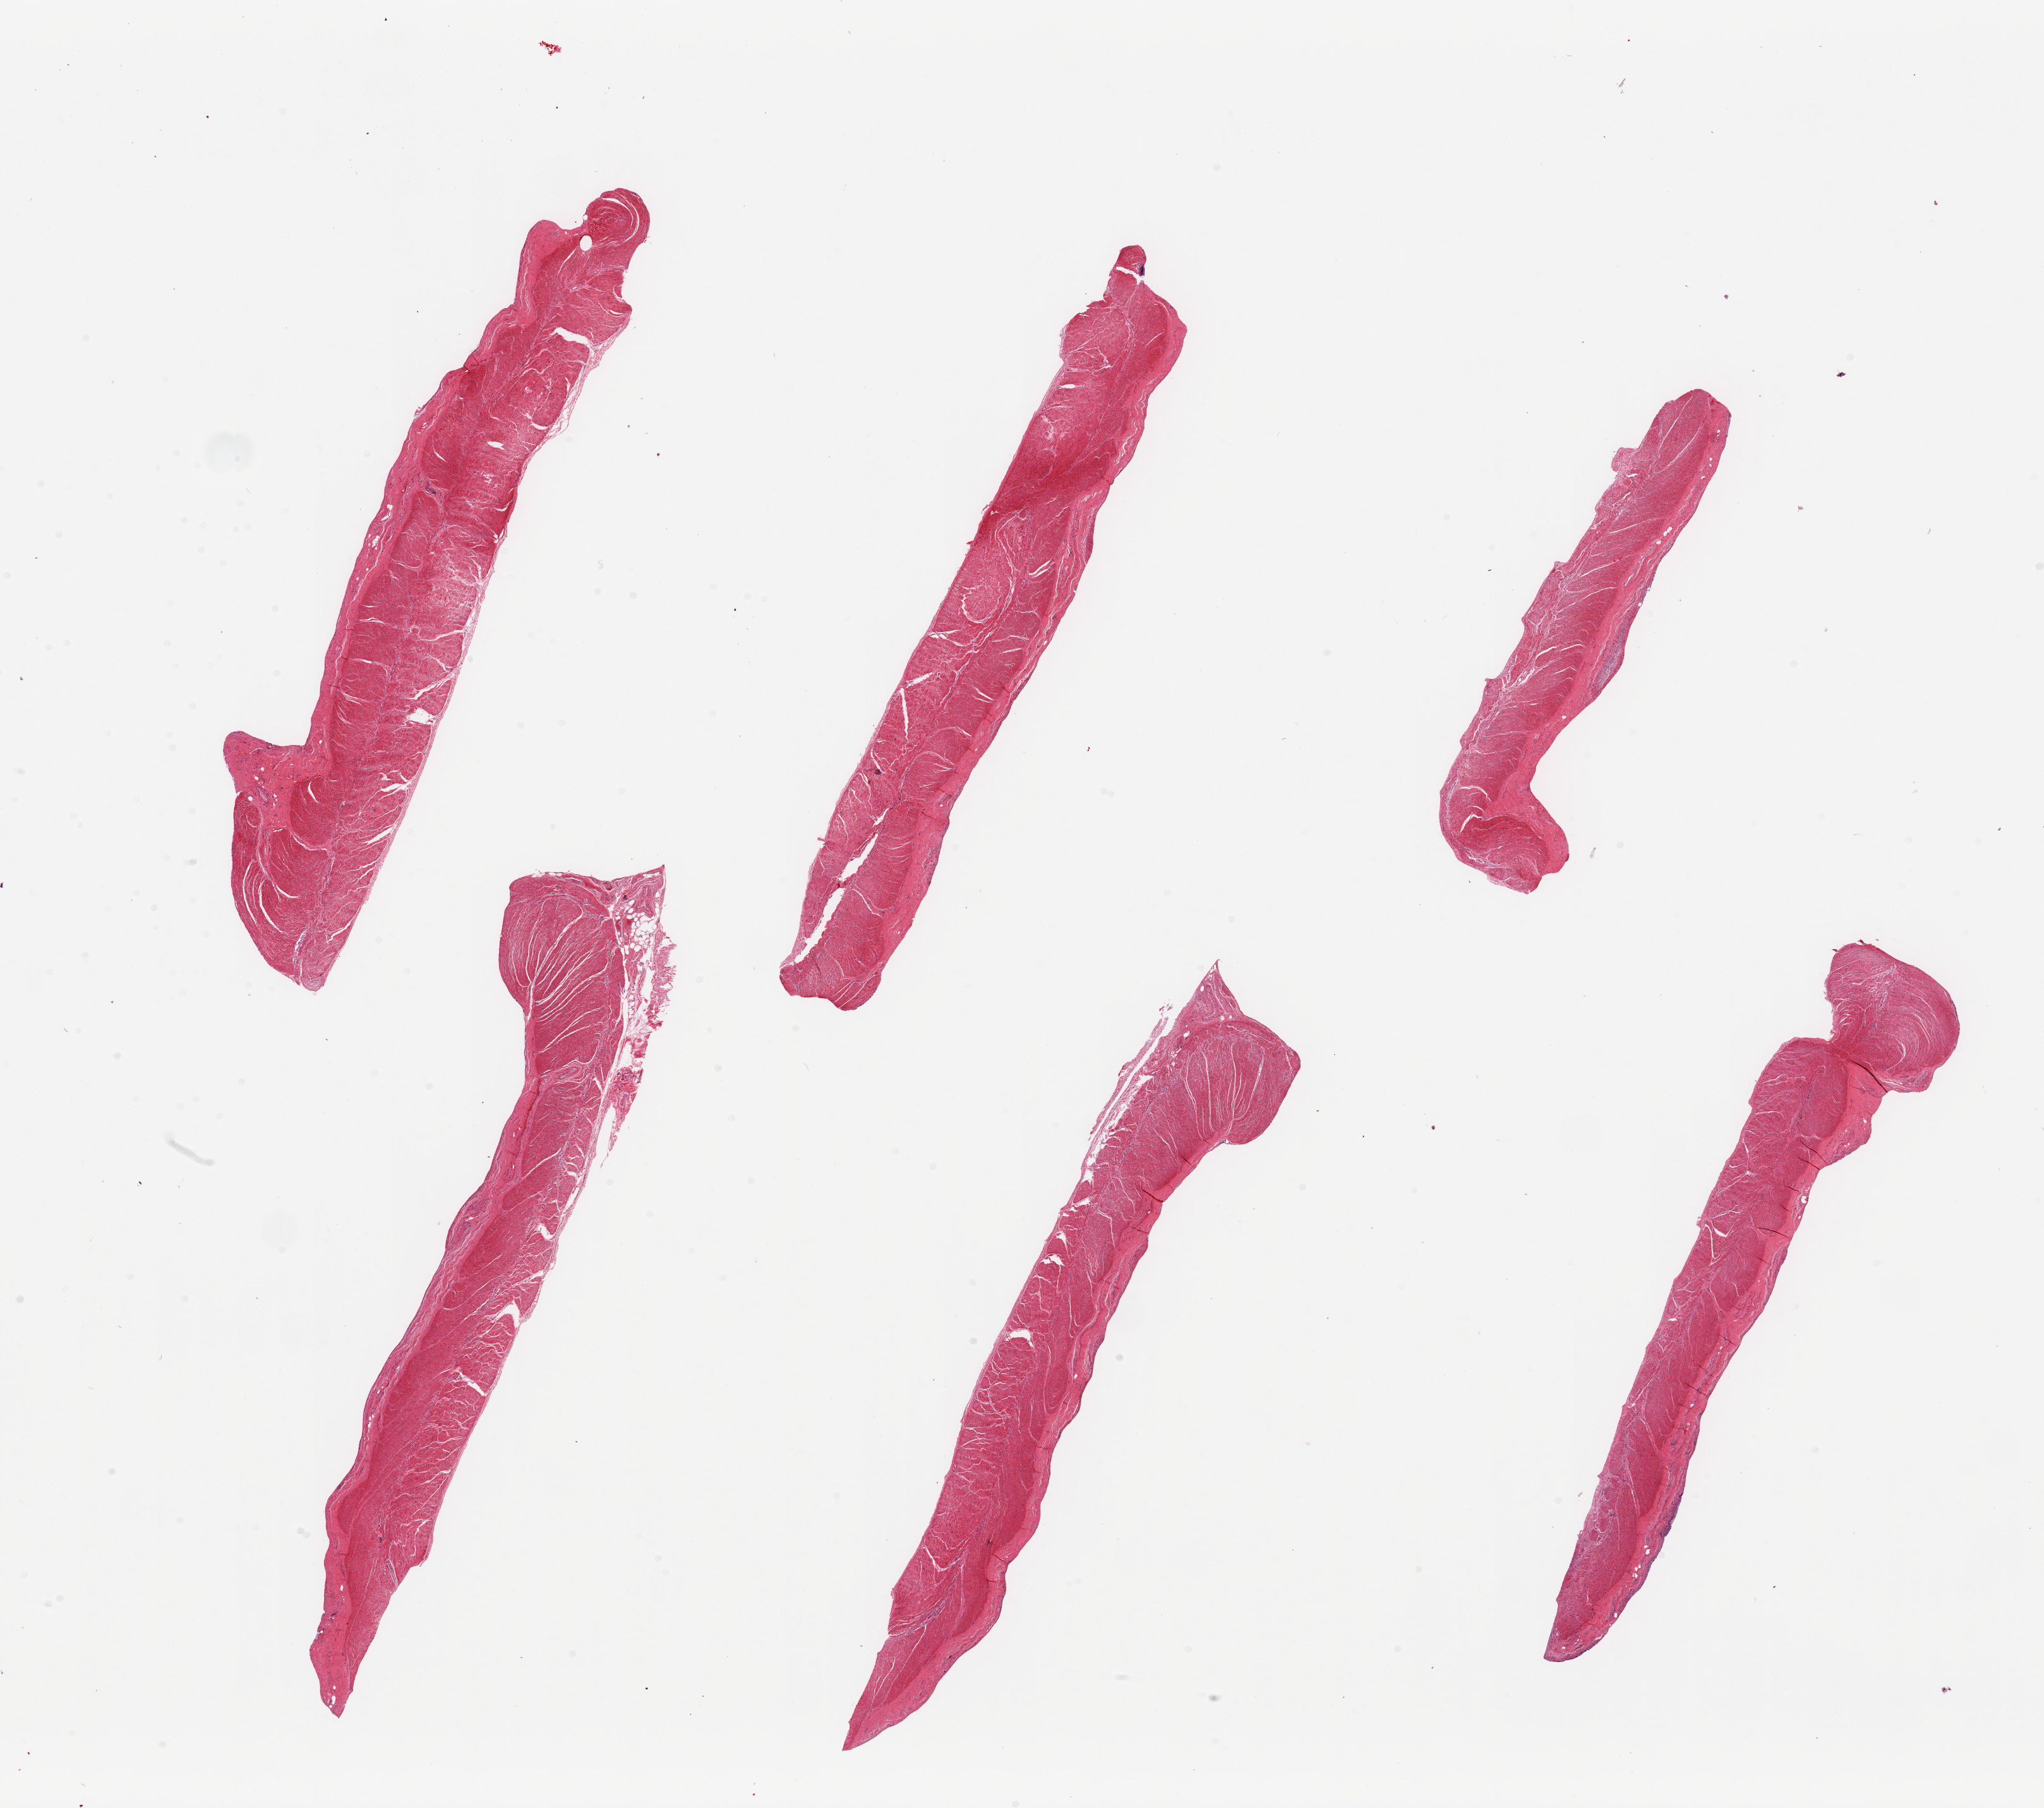
Digitized H&E-stained section — shown as a low-resolution overview of the whole scanned area (about 25.6 x 22.6 mm). PAXgene-fixed paraffin-embedded (PFPE) section. Sampled site (target tissue): sigmoid colon. Donor tissue sample.
Reviewer comment on this tissue sample: 6 pieces; essentially well trimmed target muscularis.